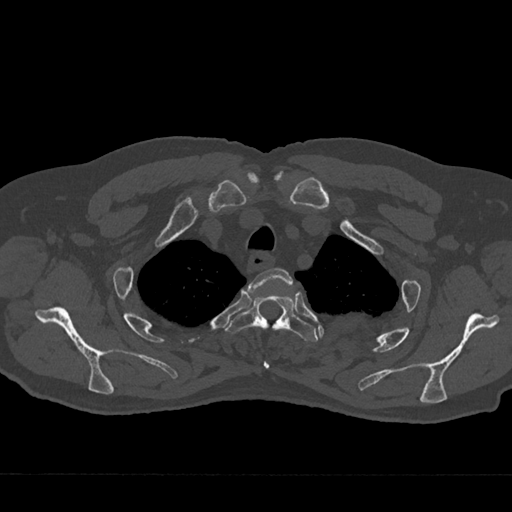
CT including the spine, one axial slice; position 581 of 797 along the scan axis; reconstruction kernel Br40s/3; 120 kVp; bone window (W 1800 / L 400 HU); 512 × 512 image matrix, field of view 377 × 377 mm. Male patient, age 75 years. From the clinical record (not read from this slice): primary cancer: renal.
Outlined on this slice (semi-automatically segmented with operator editing):
- T2 vertebra: bounding box <249,268,293,368> (left, top, right, bottom; pixels)
- T3 vertebra: <227,293,318,342>